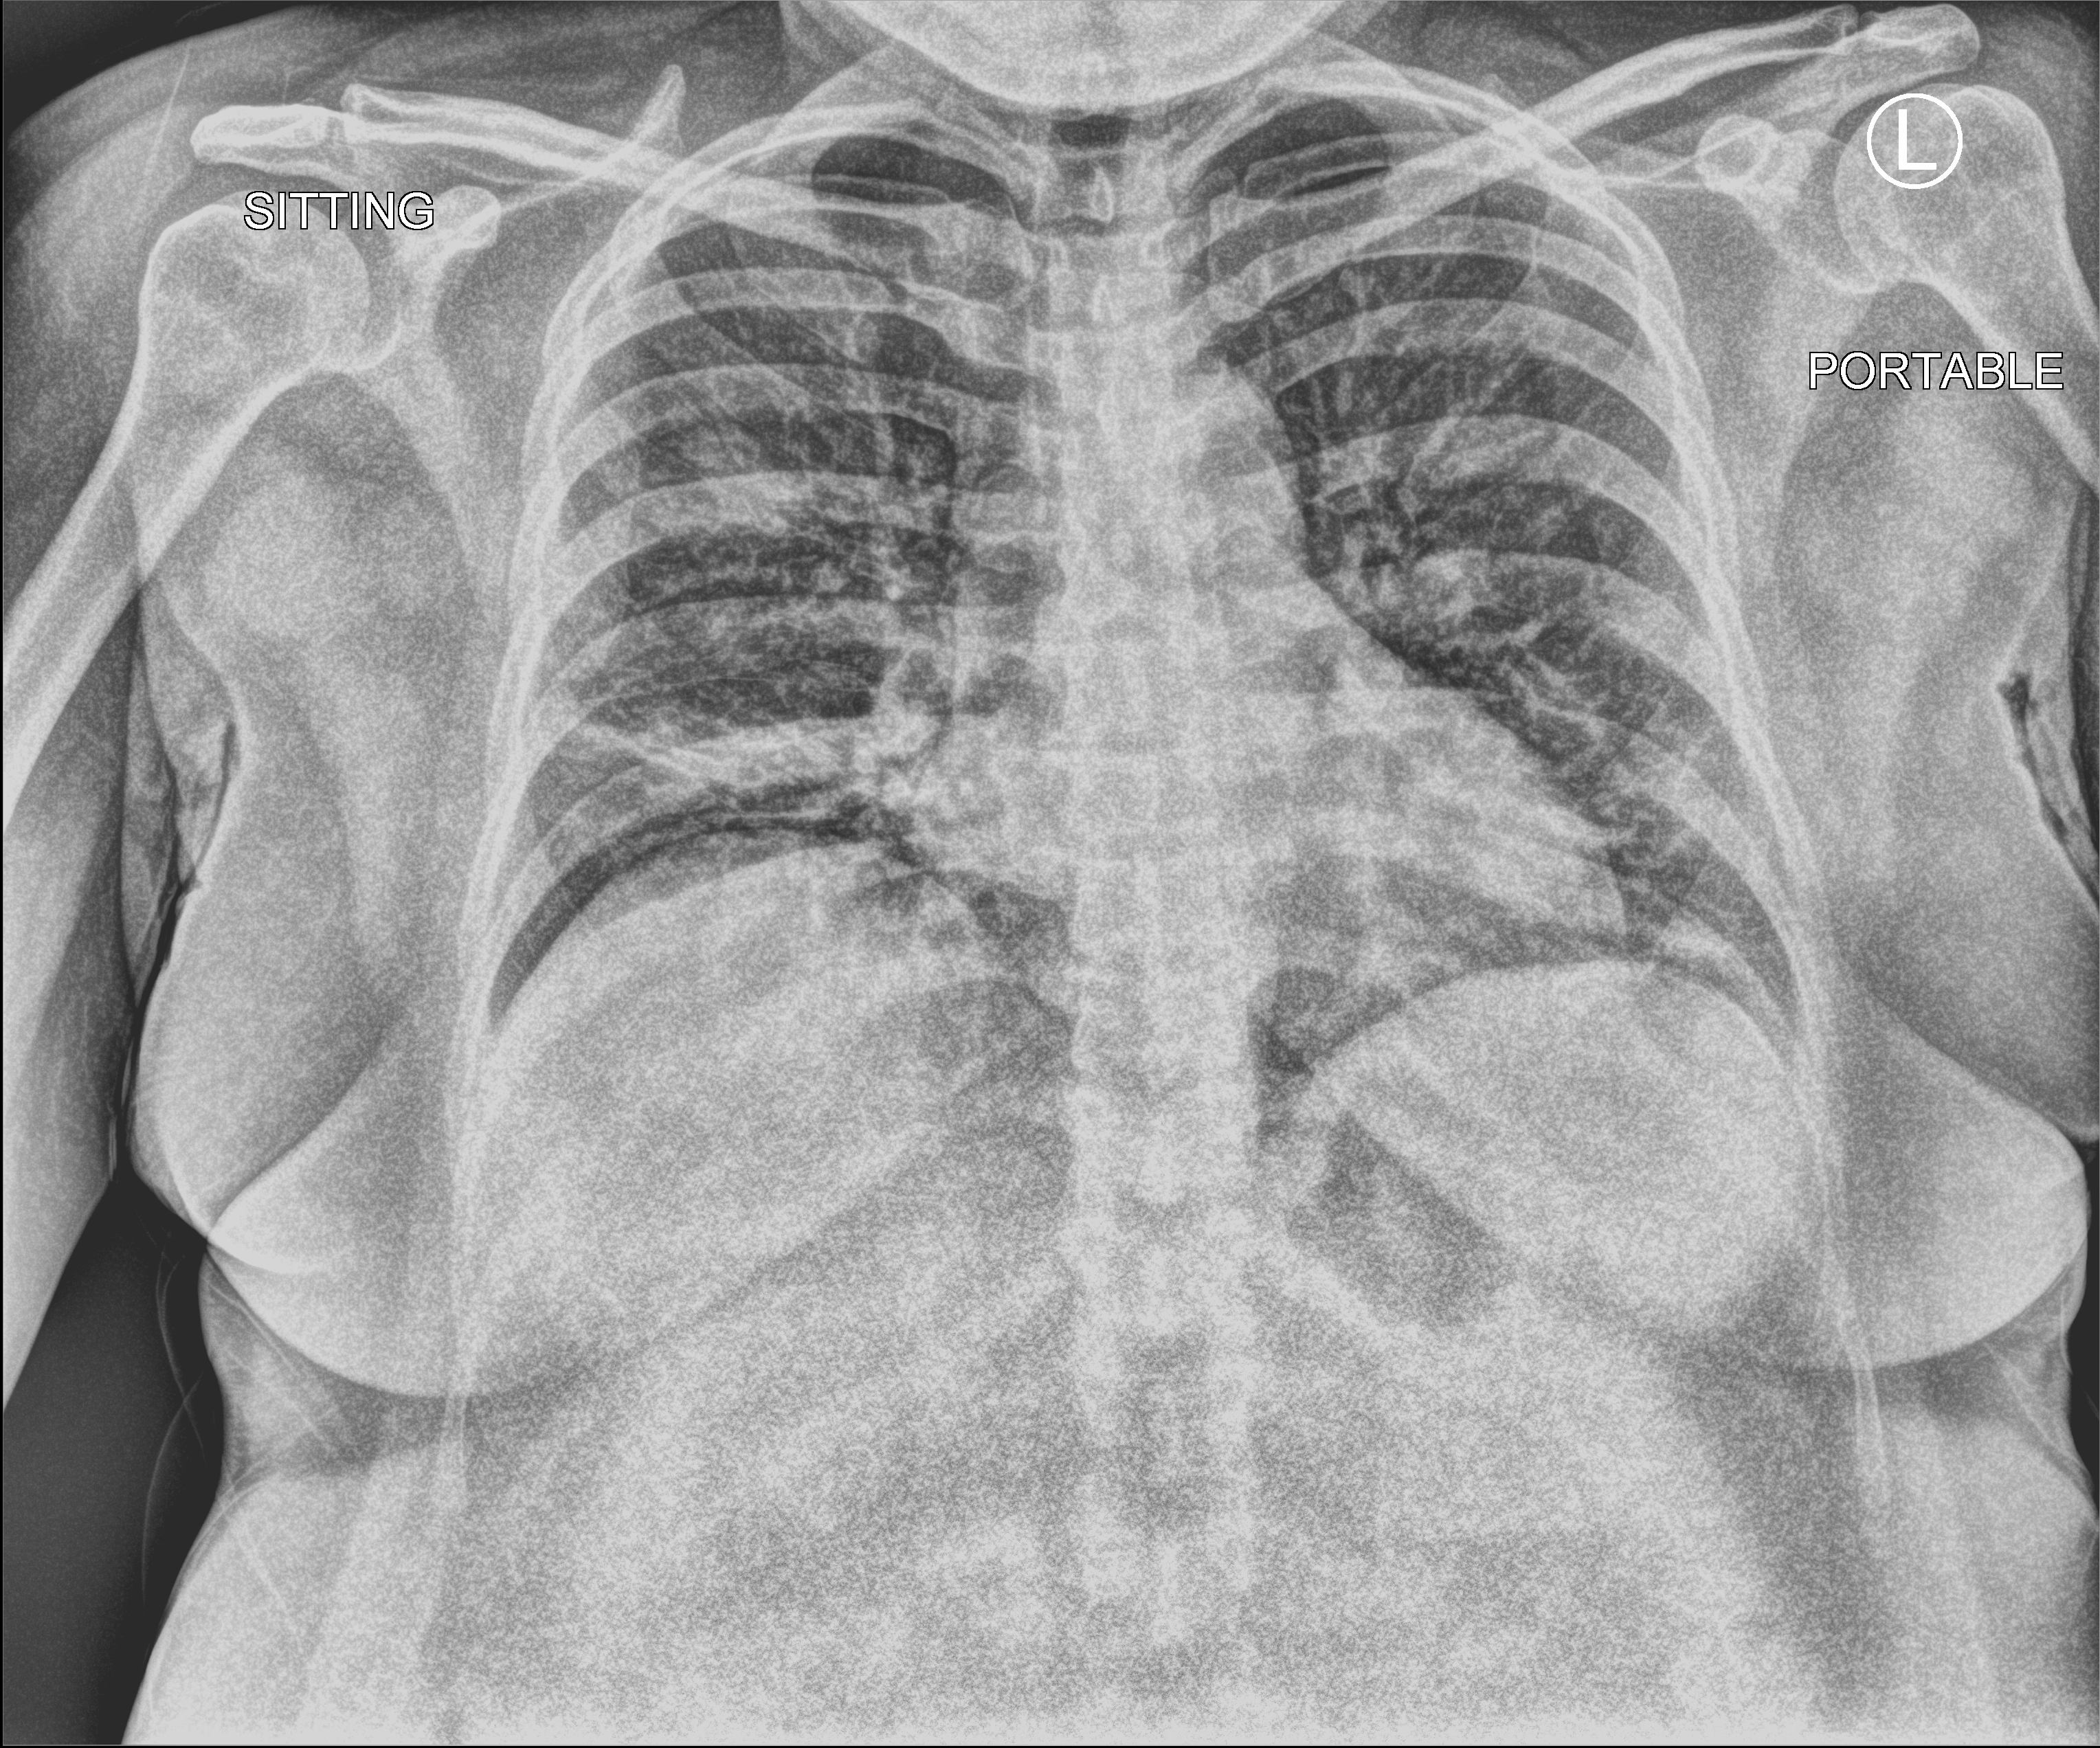
Portable chest radiograph; anteroposterior (AP) projection. Female patient hospitalised with COVID-19, age 18–59 years.
Hospital-stay facts (about this admission, not read from this image; timing relative to this image not recorded):
- other chronic lung disease (admission record): no
- admitted to intensive care during this hospital stay: no